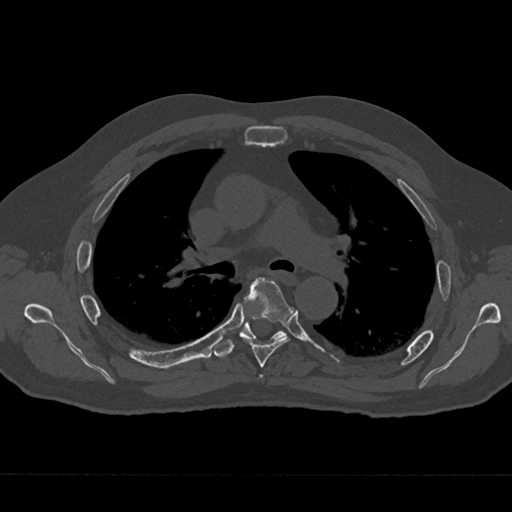
CT including the spine, one axial slice; slice 454 of 797 in the series (ordered by position); reconstruction kernel Br40s/3; bone window (W 1800 / L 400 HU); 0.5 mm slice thickness; 512 × 512 image matrix, field of view 377 × 377 mm. Male patient, age 75 years. Case-level facts recorded for this patient, not image findings: primary cancer: renal.
Structures marked on this image (semi-automatic segmentation, software-assisted and operator-edited):
- T4 vertebra: bounding box [x1, y1, x2, y2] px = [259, 375, 263, 379]
- T5 vertebra: [242, 278, 293, 368]
- T6 vertebra: [214, 313, 287, 357]